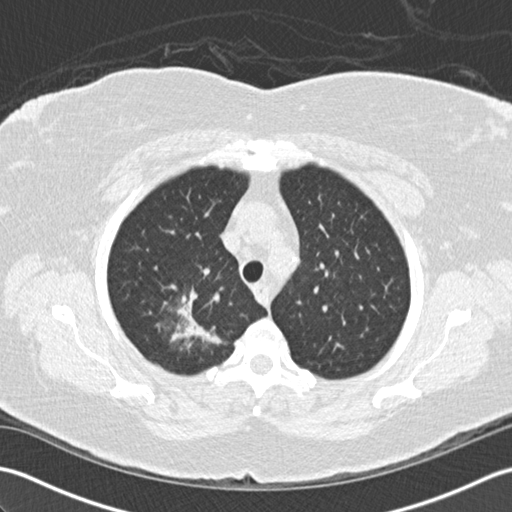
Low-dose screening chest CT, axial slice, baseline screening round, lung window (W 1500 / L -600 HU), 2 mm slice thickness, 512 × 512 image matrix, field of view 350 × 350 mm. Female participant, aged 72 years at enrolment.
- Expert-annotated lung lesion, bounding box <137,275,233,368> (left, top, right, bottom; pixels).
- The screening reader recorded 2 non-calcified nodules or masses ≥4 mm on this exam (right lower lobe, right lower lobe); which of them this box marks is not recorded.
- Lung cancer was diagnosed 494 days after this screen (after the second annual screen): bronchiolo-alveolar adenocarcinoma, NOS, right upper lobe, stage IIIB (AJCC 6th edition), 45 mm at pathology.